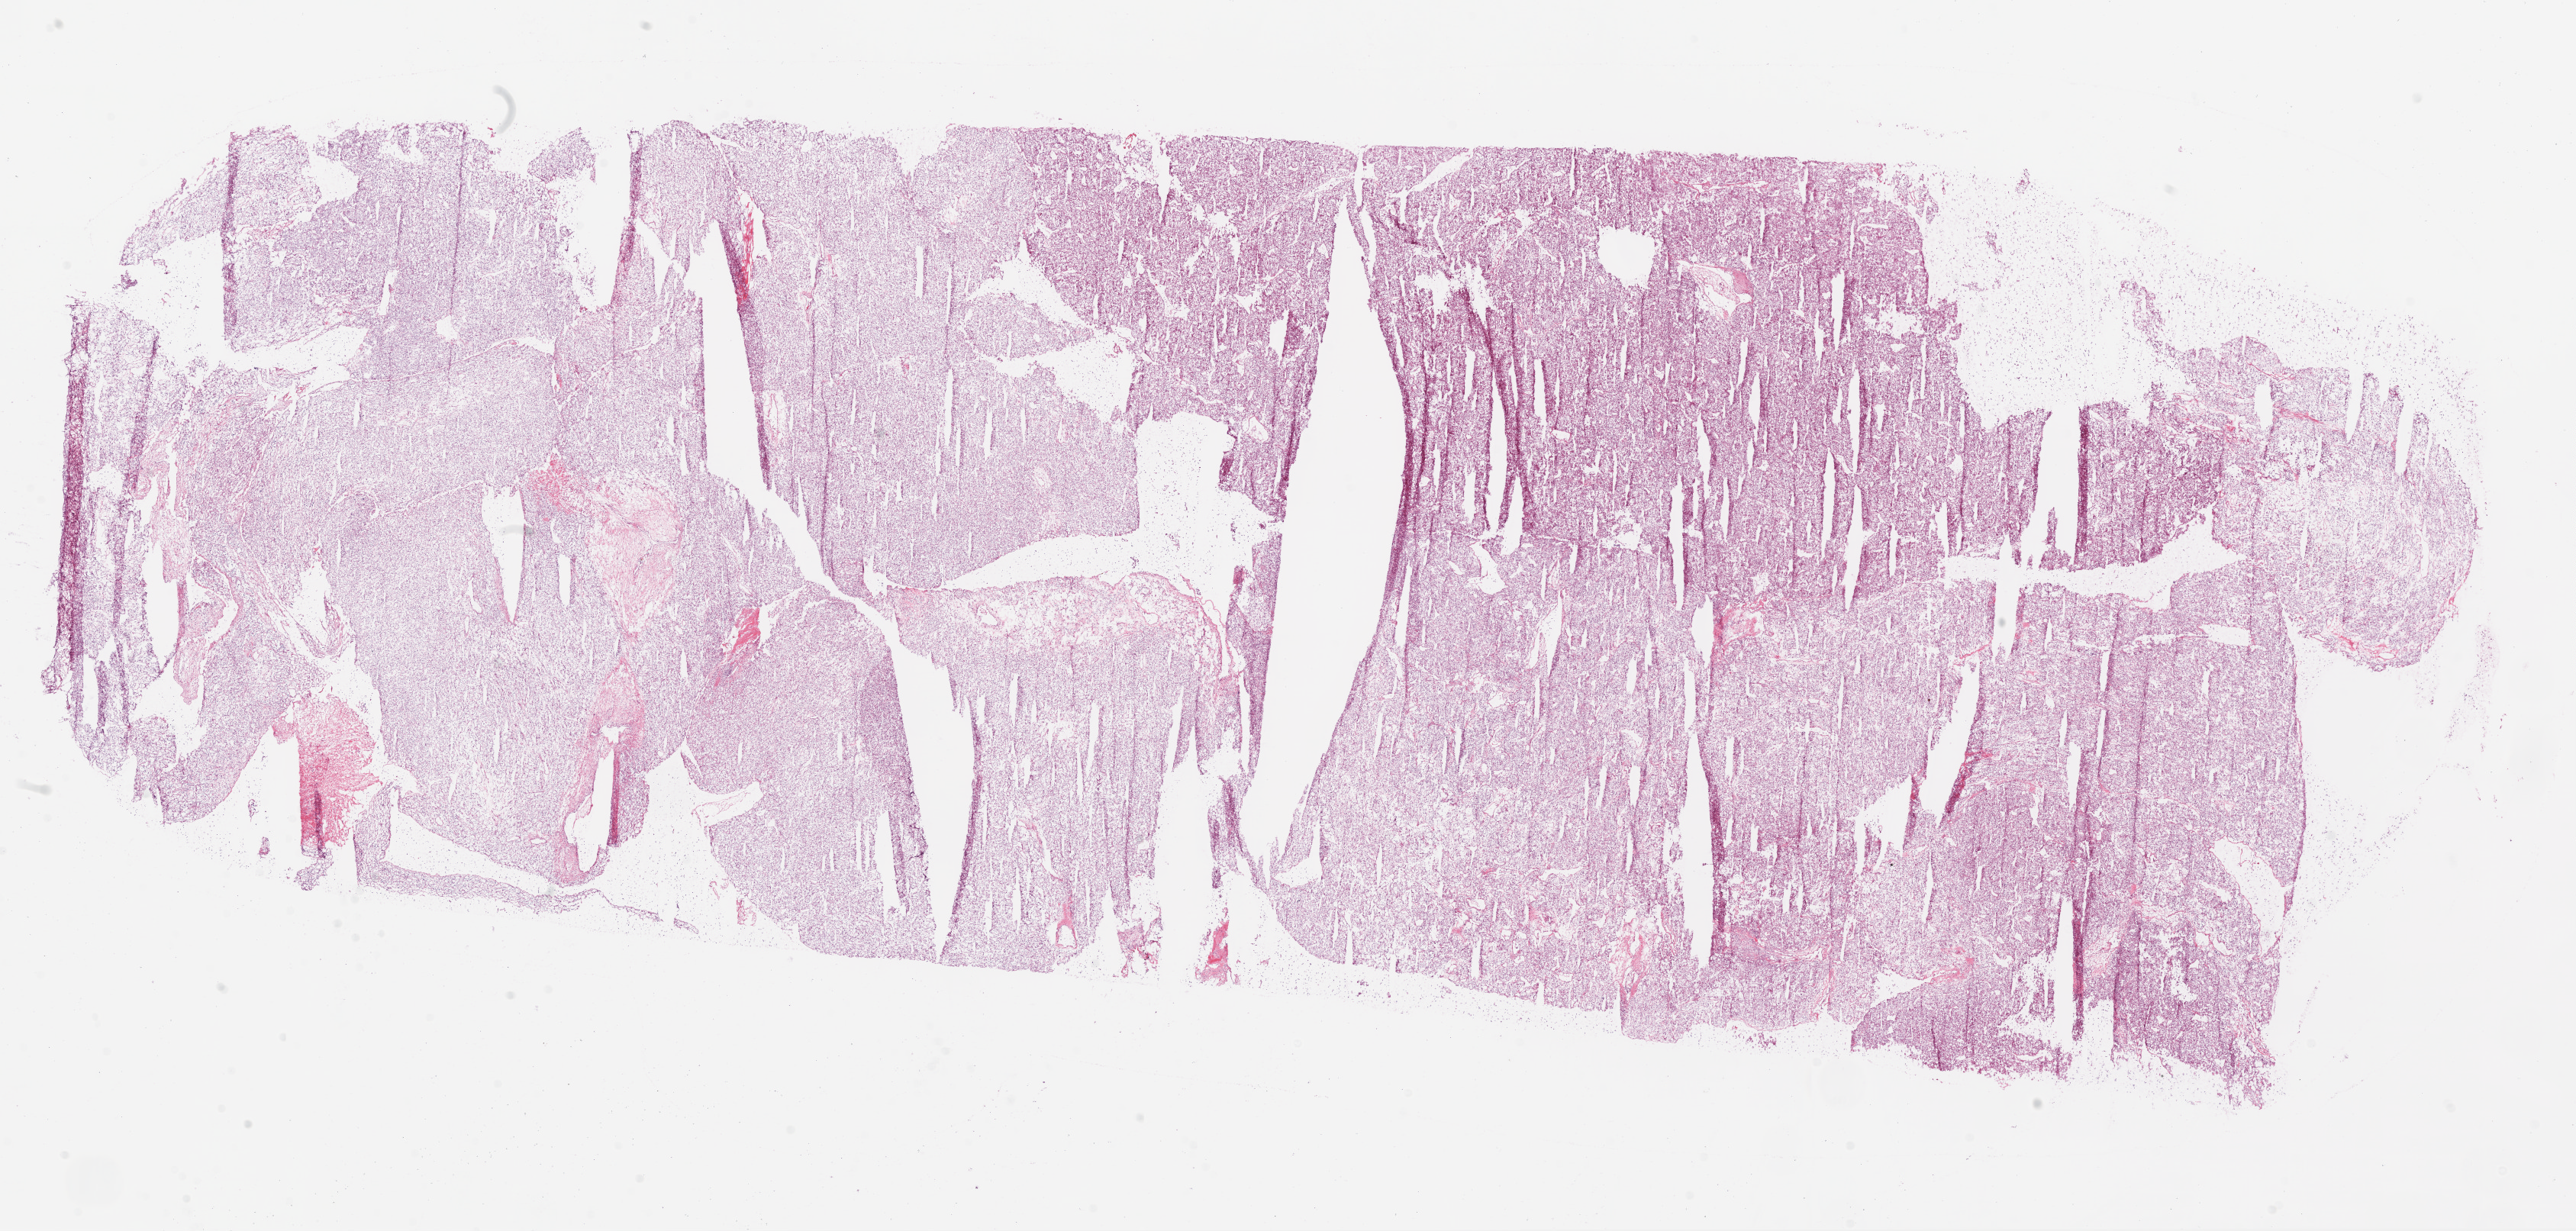
Digitized Hematoxylin and eosin (H&E) stained tissue section (whole slide) — low-resolution overview of the scanned area, about 27.1 x 12.9 mm (slide scanned at 20x). Frozen section from the bottom of the tissue portion. Sample: primary tumour, kidney. Female, age 48 years at initial diagnosis. Histologic grade: G3 (poorly differentiated). Composition of this section per pathologist review: tumour cells 95%, tumour nuclei 85%, normal cells 0%, stromal cells 5%, necrosis 0%.
Pathologic diagnosis: Clear cell adenocarcinoma, NOS. AJCC pathologic stage: IV. TNM: T3a N0 M1.